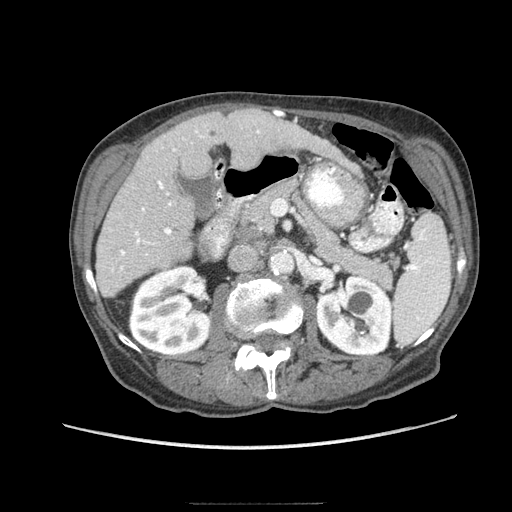
Contrast-enhanced abdominal CT (liver protocol), one axial slice; slice 36 of 83 in the series (ordered by position); reconstruction kernel STANDARD; 140 kVp; soft-tissue window (W 400 / L 40 HU); 2.5 mm slice thickness; 512 × 512 image matrix, field of view 360 × 360 mm. Case-level facts recorded for this patient, not image findings: diagnosis: hepatocellular carcinoma (patient treated with transarterial chemoembolisation; whether this scan precedes or follows treatment is not stated here); TNM stage (as recorded): Stage-I; Child-Pugh class: A; tumour differentiation: moderately differentiated.
Annotated regions visible in this slice (semi-automatically segmented with operator editing):
- liver parenchyma outside the tumour (the mass and vessels are separate outlines, so this box may not span the whole liver): bounding box (x1, y1, x2, y2) in pixels: (96, 108, 328, 296)
- liver vessels: (111, 130, 259, 271)